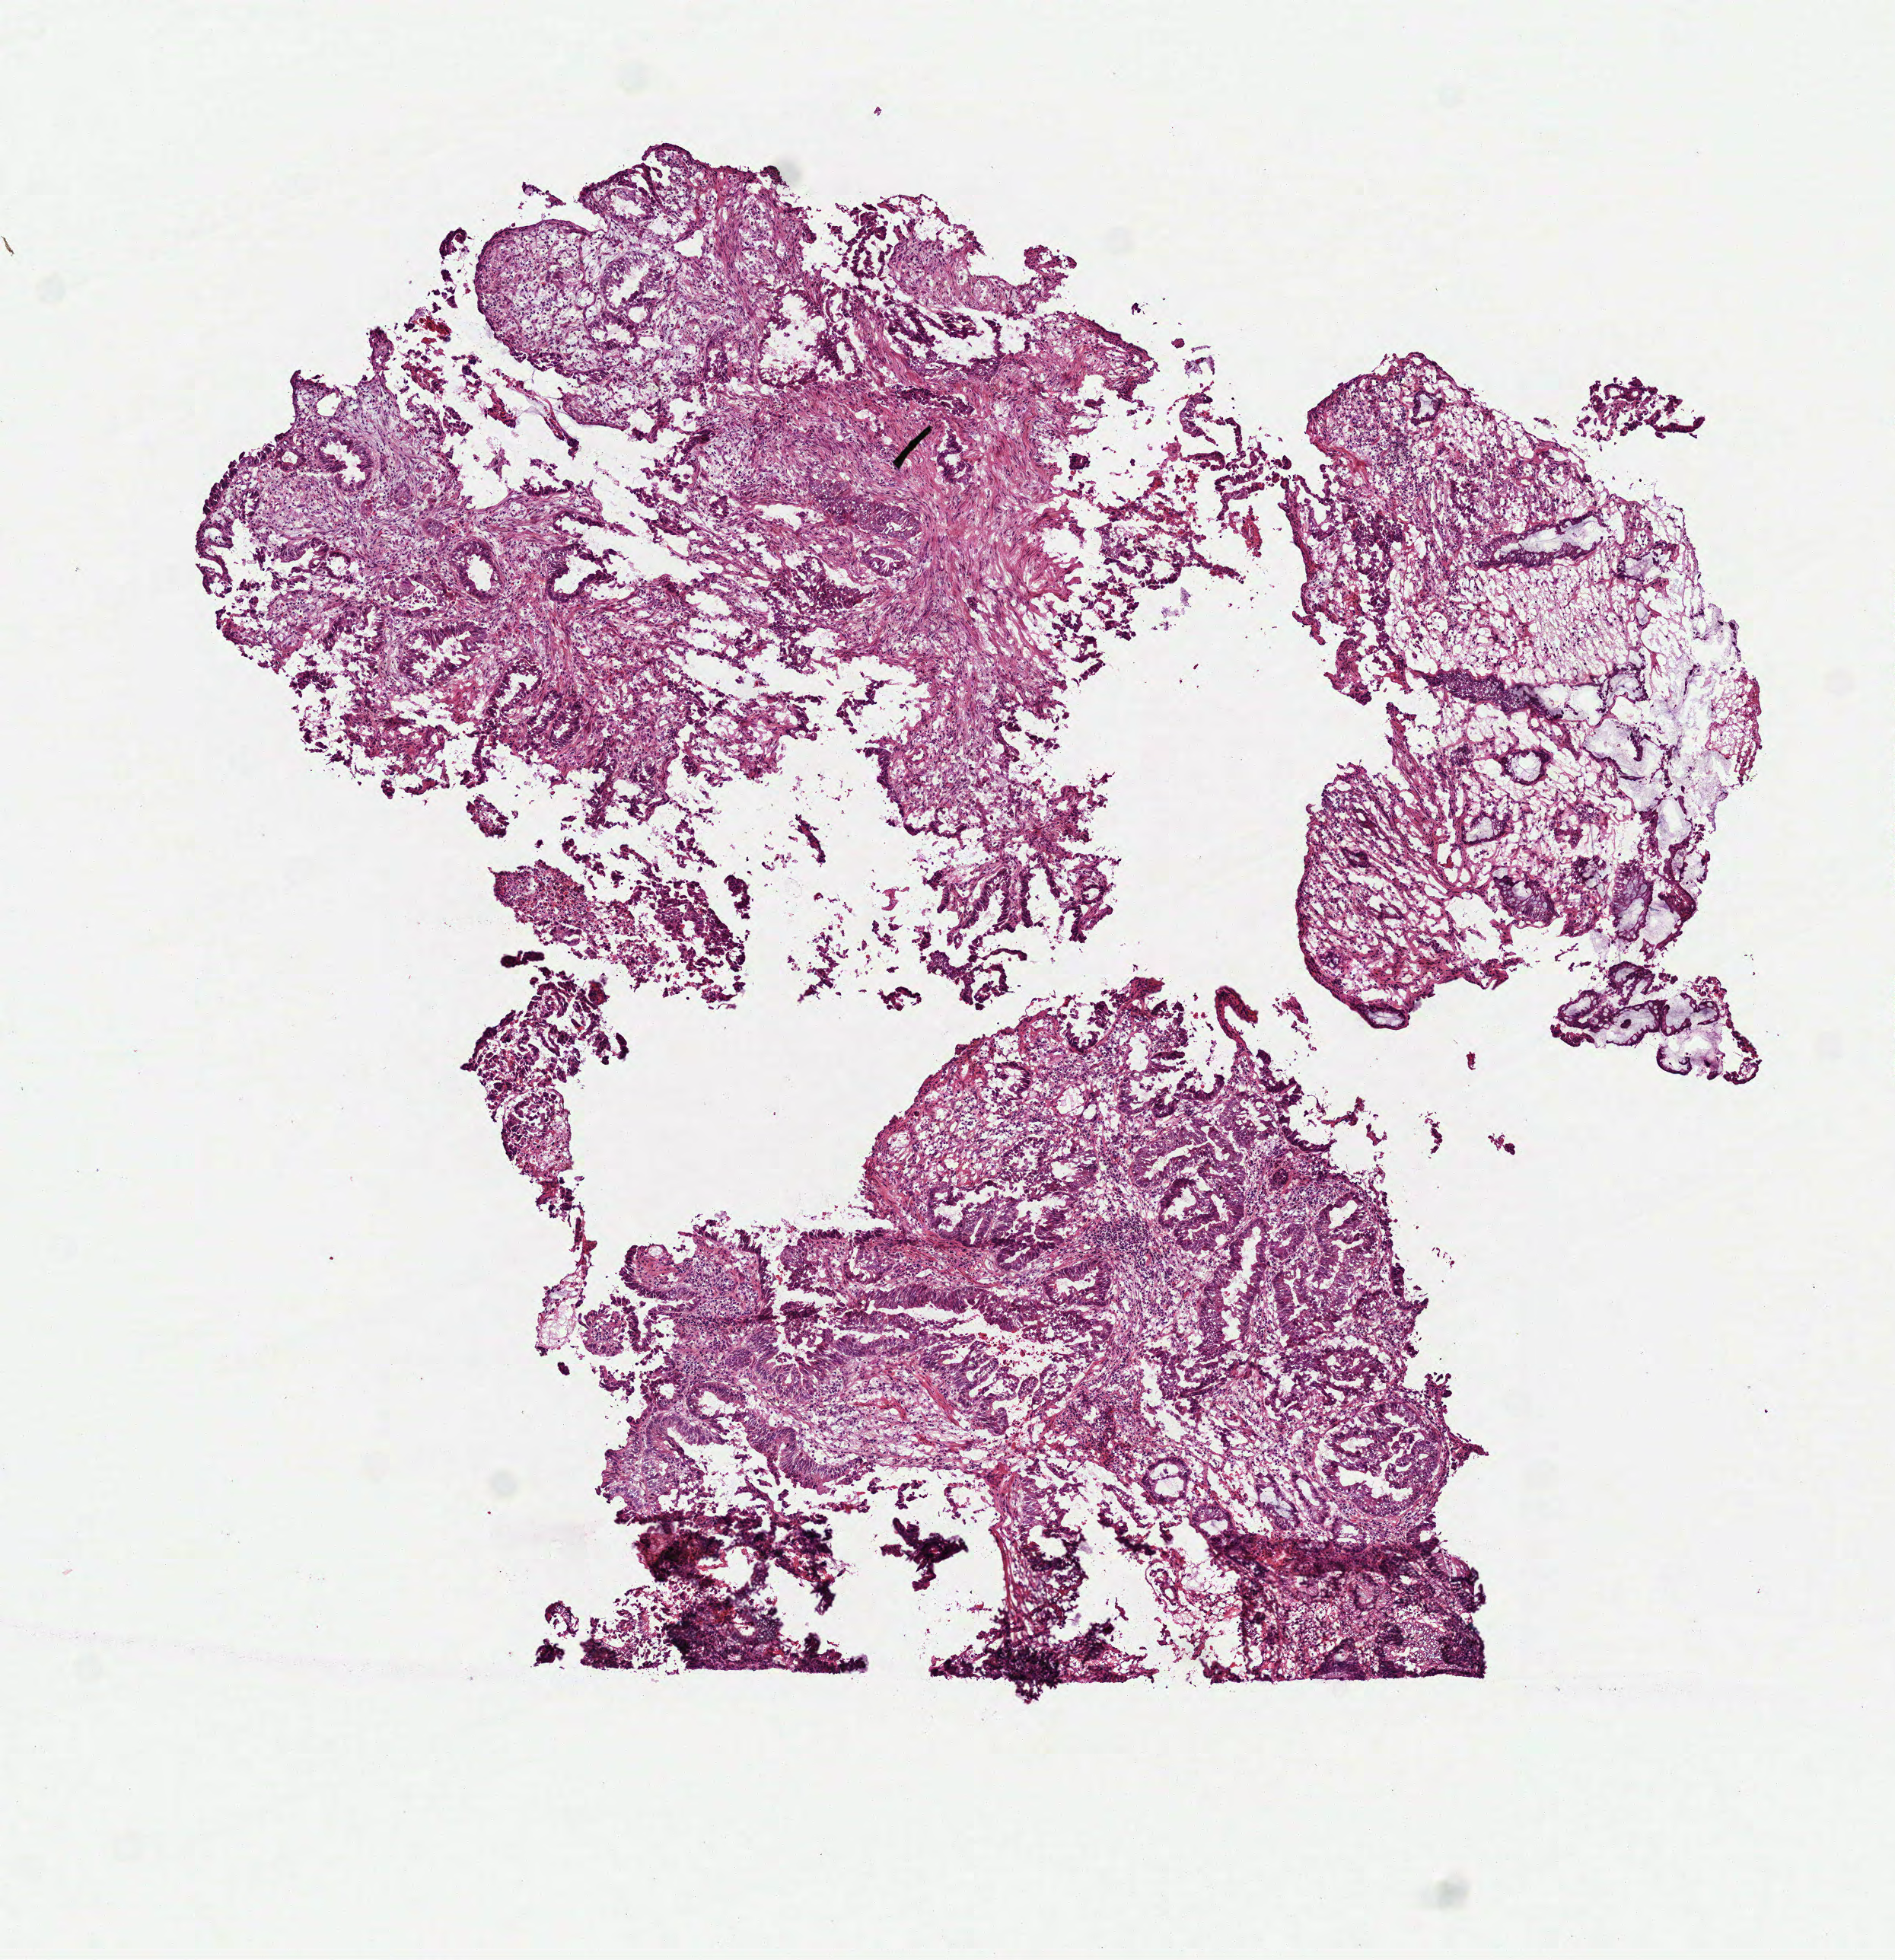
Hematoxylin and eosin (H&E) stained whole-slide image, low-resolution overview of the scanned area, about 5.0 x 5.2 mm (slide scanned at 40x). Frozen section from the top of the tissue portion. Rectum, primary tumour sample. Female patient; age at initial diagnosis 53 years. Pathologist review of this section (percent, as recorded): tumour cells 55%, tumour nuclei 65%, normal cells 15%, stromal cells 25%, necrosis 5%.
* diagnosis: Adenocarcinoma, NOS
* AJCC pathologic stage: I (7th edition)